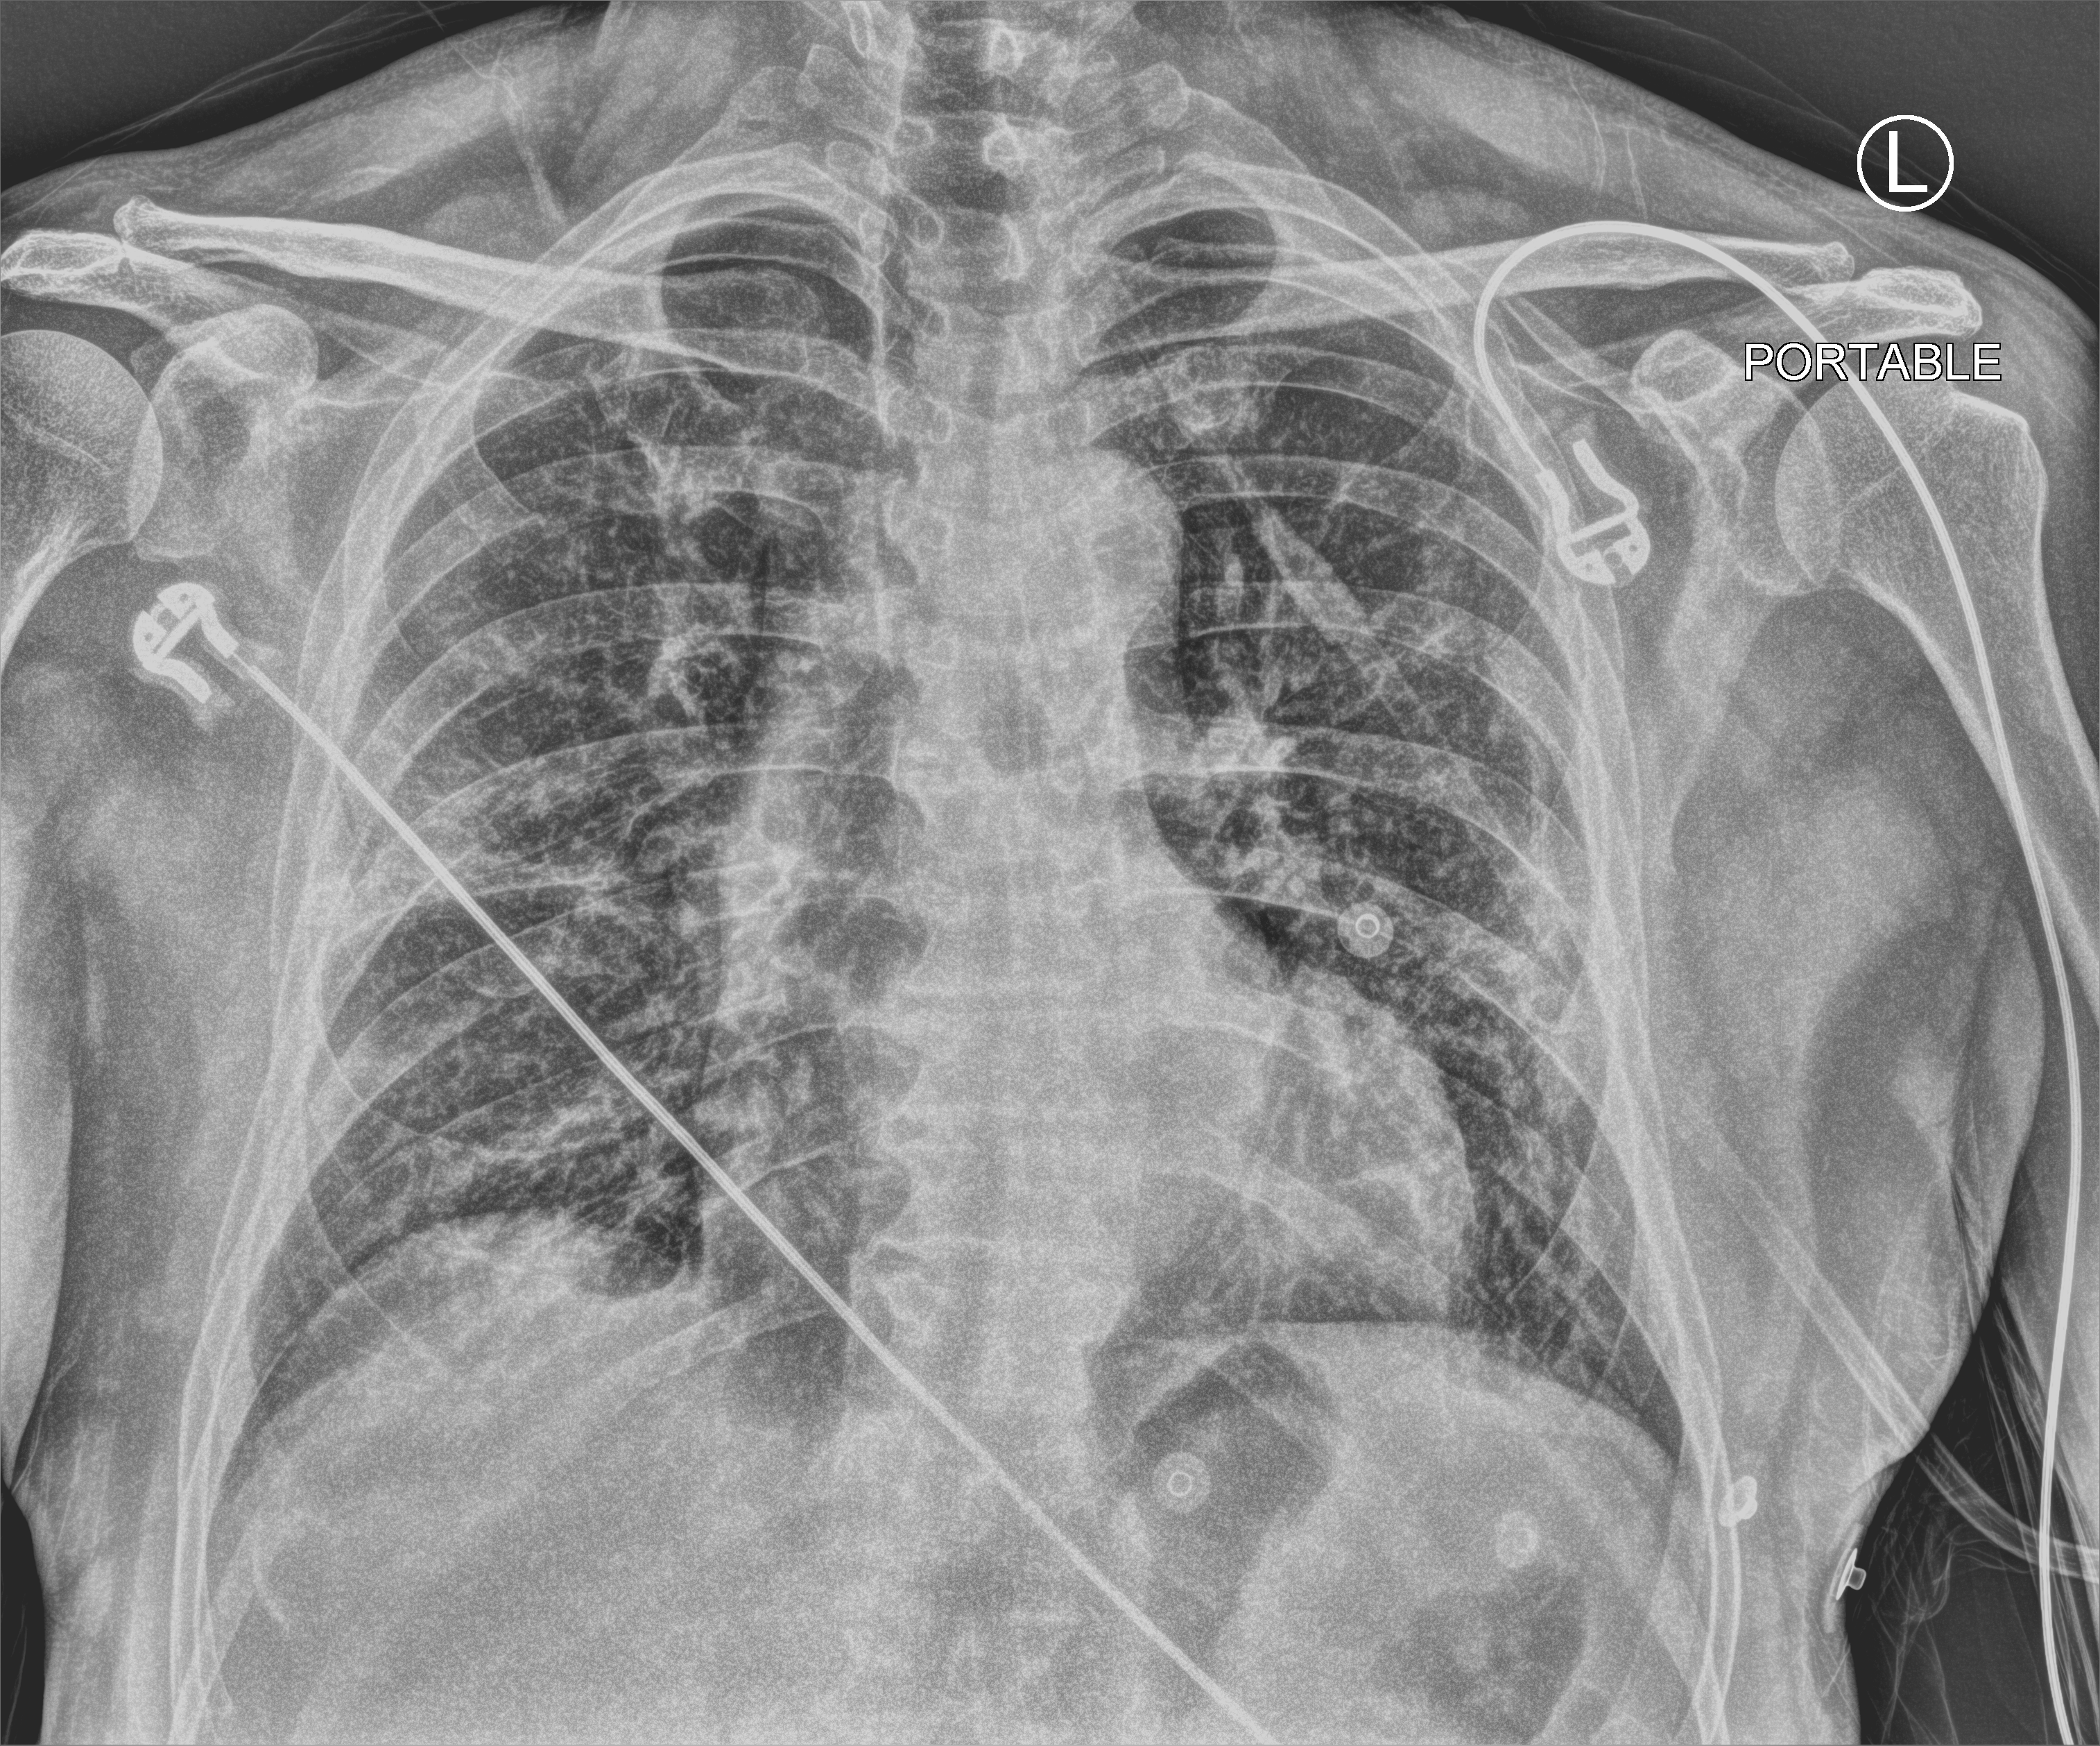
Bedside chest radiograph (computed radiography), anteroposterior (AP) projection. Patient hospitalised with COVID-19; male, aged 60–74 years.
From the hospital-stay record, not from the radiograph (when in the stay this image was taken is not recorded): admitted to intensive care during this hospital stay: no.